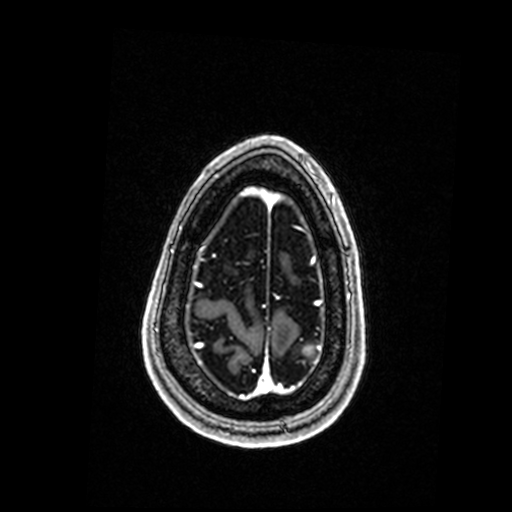
Brain MRI from a brain-tumour surgery series, one axial slice; position 35 of 192 along the scan axis; T1-weighted post-contrast; 0.98 mm slice thickness; 512 × 512 image matrix, field of view 250 × 250 mm. Case-level facts recorded for this patient, not image findings: histopathology: Metastastic Carcinoma, Poorly Differentiated; tumour location: Left Parietal.
Annotated regions visible in this slice (outlined manually by an expert reader):
- tumour: bounding box <315,355,319,361> (left, top, right, bottom; pixels)